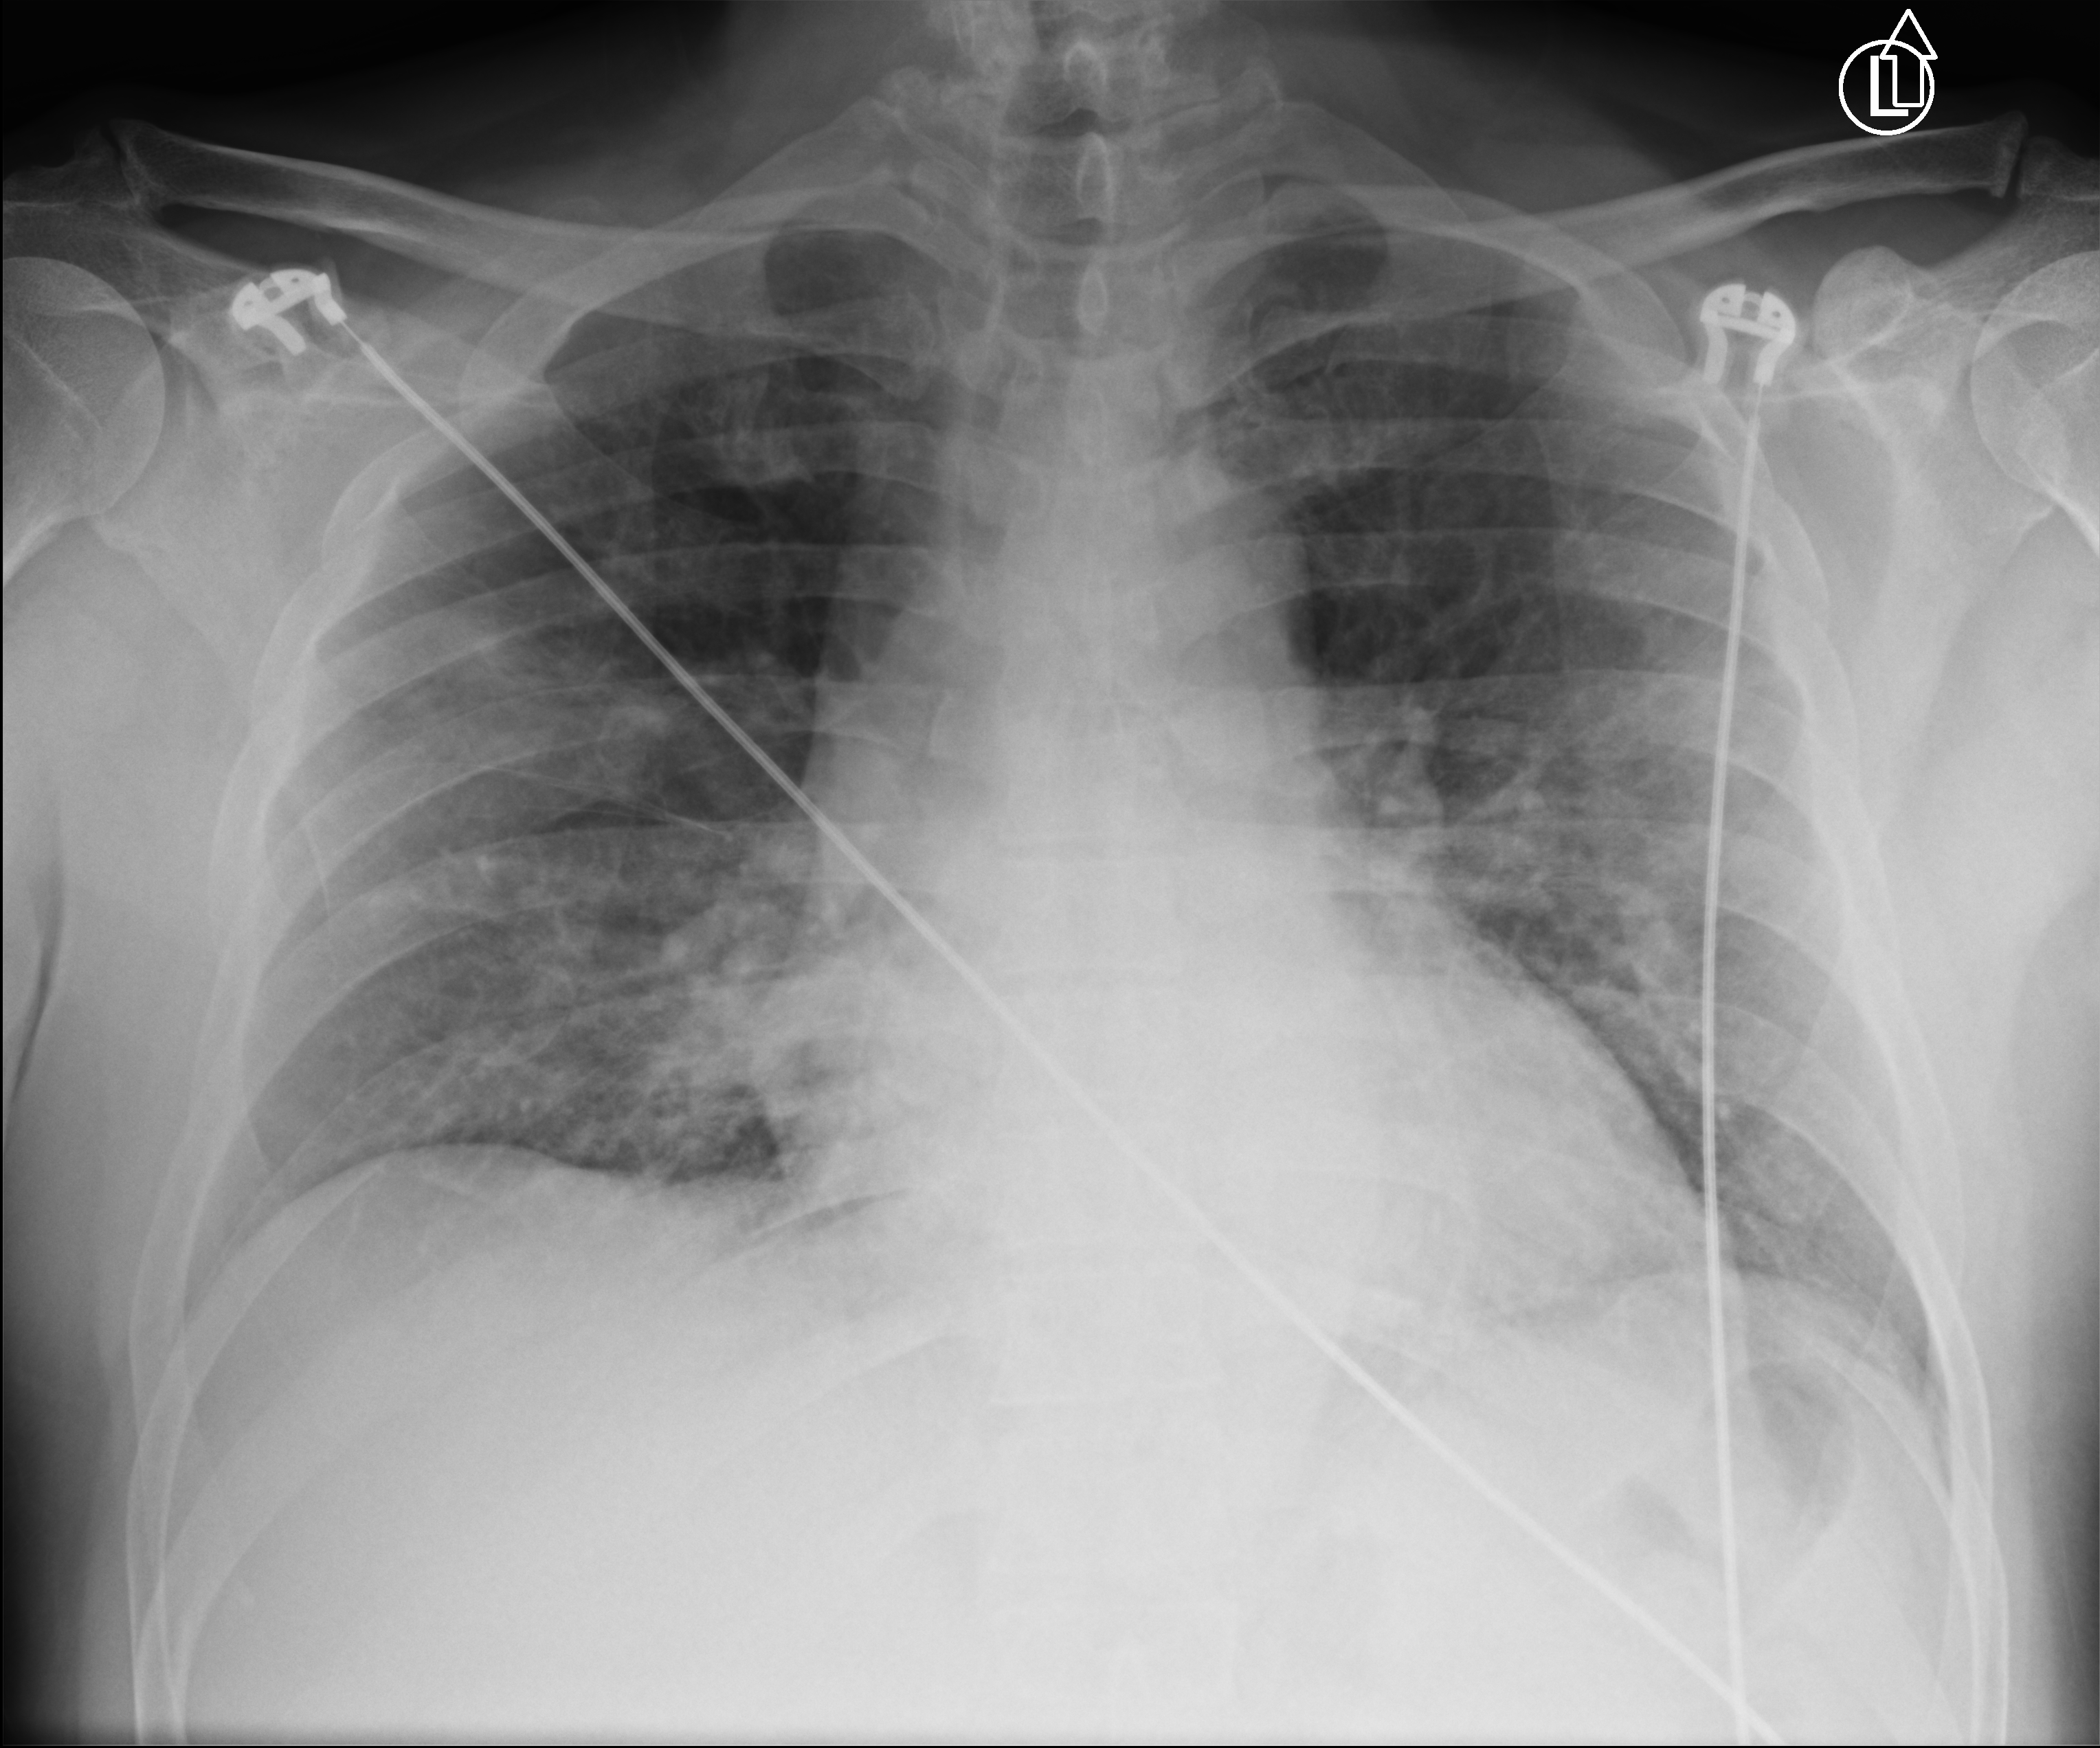
Chest X-ray (portable), anteroposterior (AP) projection. Patient hospitalised with COVID-19; male, aged 60–74 years.
Admission-level facts for this patient (not findings on this image; timing relative to this image not recorded):
- hypertension (admission record): no